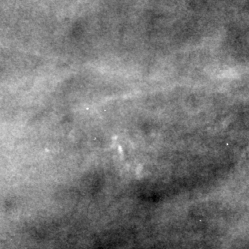
Region of interest cut from a scanned film mammogram (one marked finding), right breast, MLO view.
- Finding: calcifications, morphology pleomorphic, distribution clustered; BI-RADS assessment category 4; subtlety rating 3 on a 1 (subtle) to 5 (obvious) scale; pathology result (as recorded, not read from the image): benign.